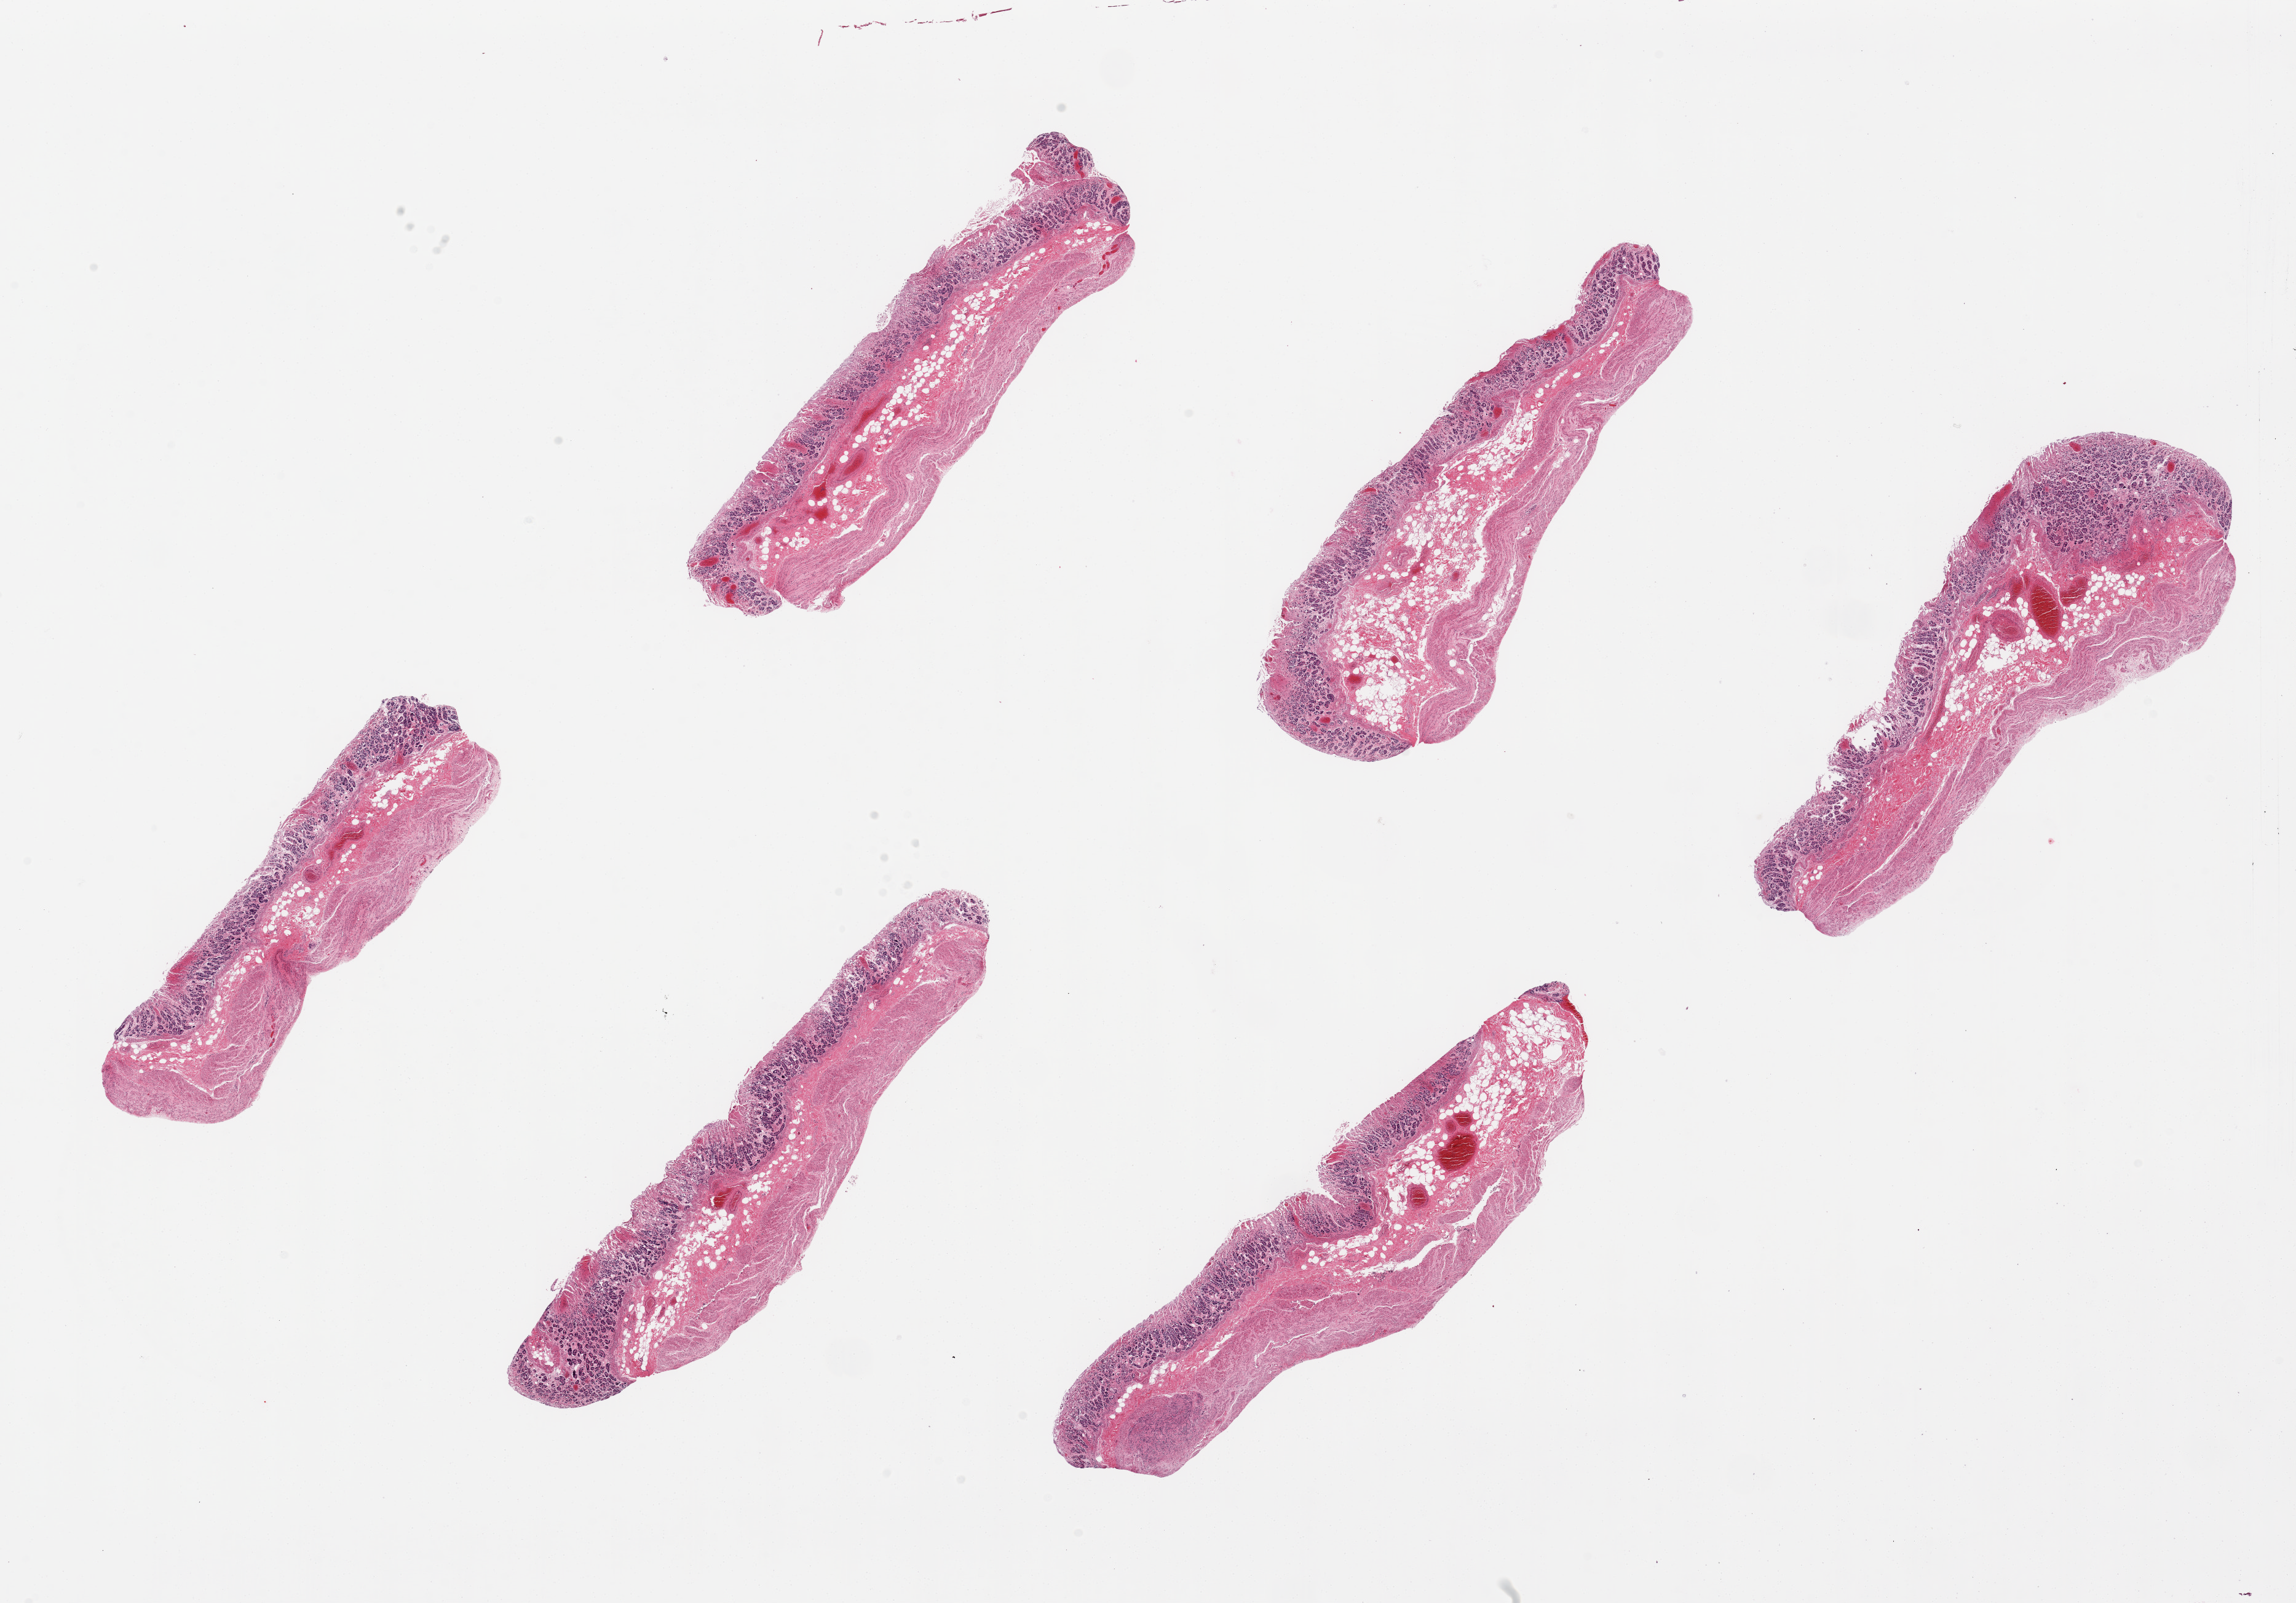
Whole-slide image, H&E stain — a low-resolution overview of the entire scanned area, about 29.5 x 20.6 mm; PAXgene-fixed, paraffin-embedded tissue; target tissue: stomach; tissue donor sample. Donor: male.
Reviewer comment on this tissue sample: 6 pieces. up to 9x2mm; mucosa is ~30% thickness but poorly preserved.